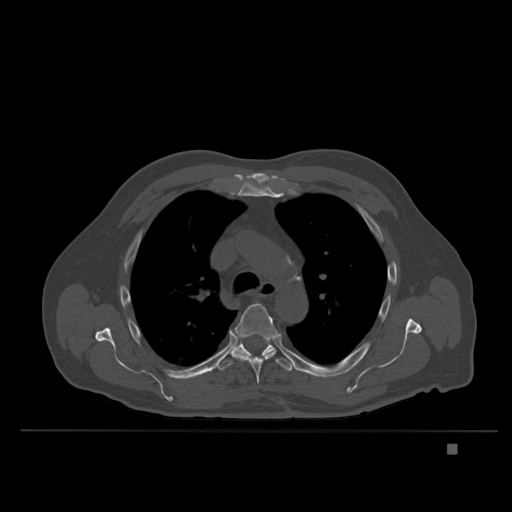
CT including the spine, one axial slice. Bone window (W 1800 / L 400 HU). 512 × 512 image matrix, field of view 434 × 434 mm. Male patient, age 73 years. From the clinical record (not read from this slice): primary cancer: skin.
Structures marked on this image (semi-automatic segmentation, software-assisted and operator-edited):
- T5 vertebra: box from (x=231, y=303) to (x=281, y=384) px
- T6 vertebra: (x=217, y=340)–(x=293, y=371)
- T7 vertebra: (x=236, y=339)–(x=239, y=345)